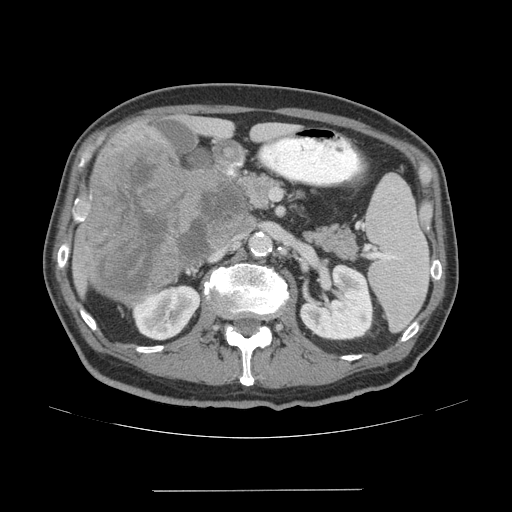
Contrast-enhanced abdominal CT (liver protocol), one axial slice. Slice 20 of 77 in the series (ordered by position). Soft-tissue window (W 400 / L 40 HU). 2.5 mm slice thickness. 512 × 512 image matrix, field of view 400 × 400 mm. Case-level facts recorded for this patient, not image findings: diagnosis: hepatocellular carcinoma (patient treated with transarterial chemoembolisation; whether this scan precedes or follows treatment is not stated here); TNM stage (as recorded): Stage-IVA; Child-Pugh class: A; tumour differentiation: well differentiated; tumour nodularity: uninodular.
Structures marked on this image (semi-automatic segmentation, software-assisted and operator-edited):
- liver parenchyma outside the tumour (the mass and vessels are separate outlines, so this box may not span the whole liver): bounding box <72,122,291,305> (left, top, right, bottom; pixels)
- mass: <84,140,248,303>
- liver vessels: <77,216,85,221>